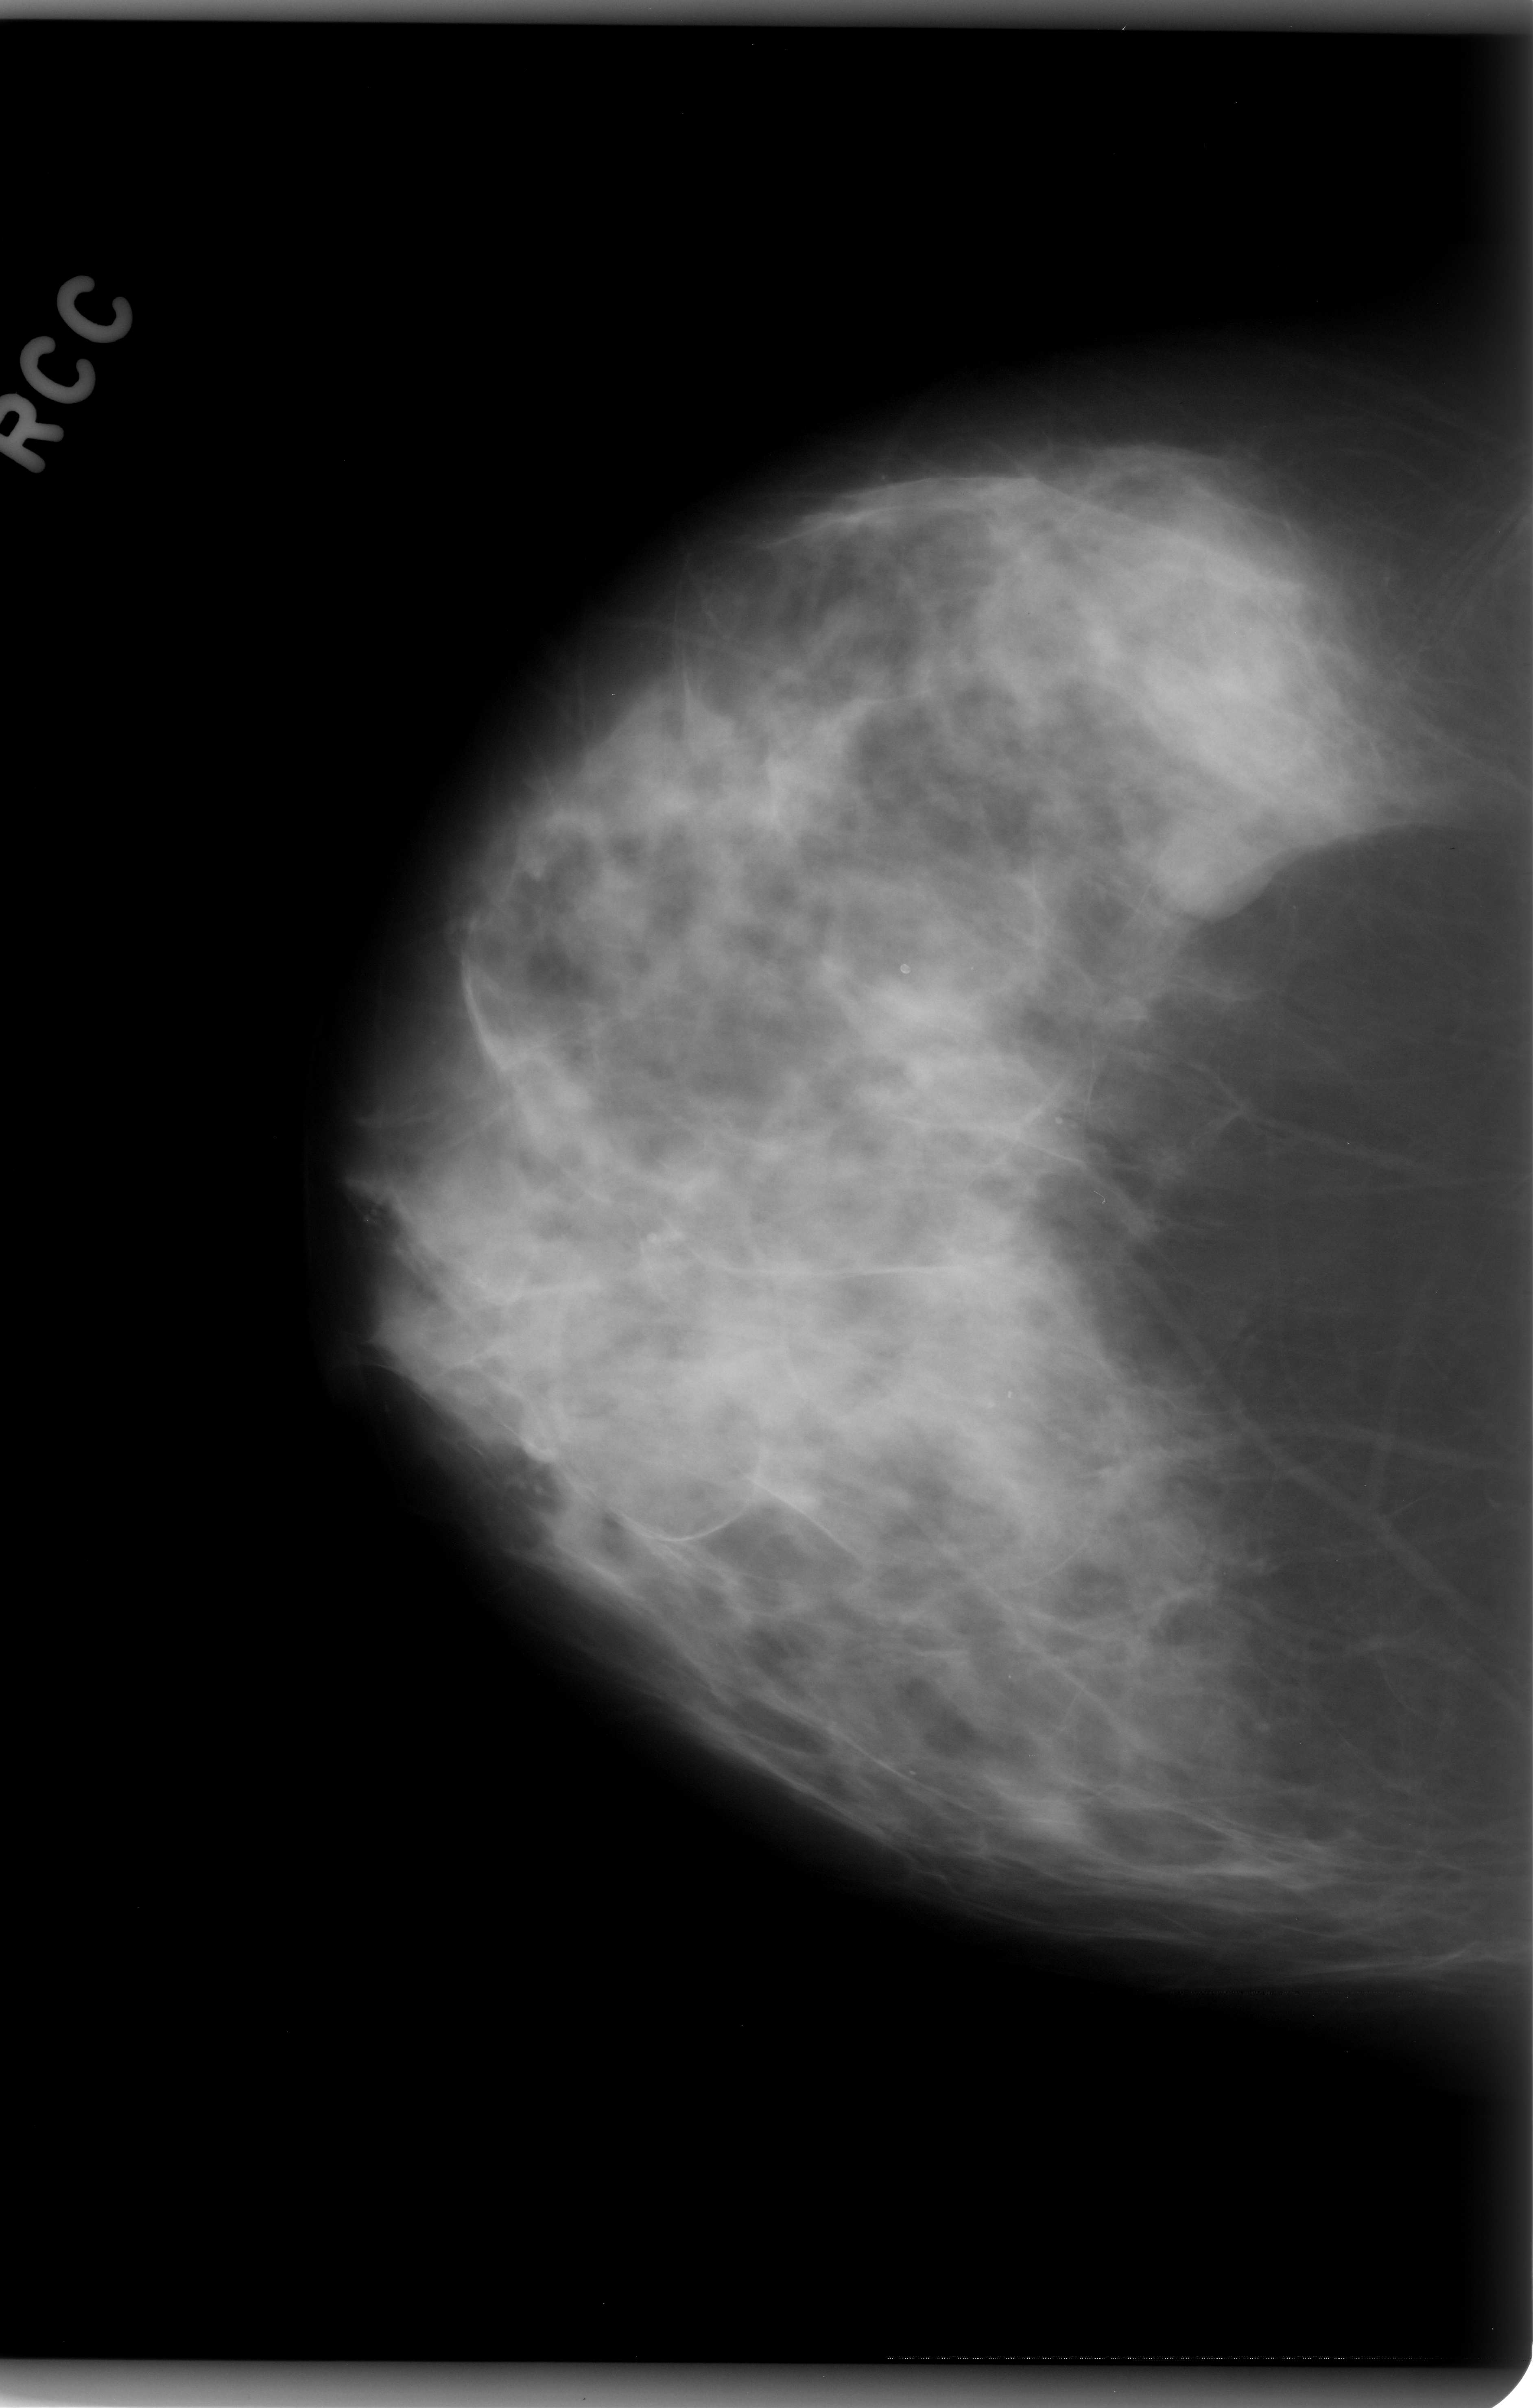
Scanned film-screen mammogram, right breast, CC view, BI-RADS breast density category 3 (scale 1–4).
Finding: mass, shape oval, margins circumscribed; BI-RADS assessment category 4; subtlety rating 5 on a 1 (subtle) to 5 (obvious) scale; pathology (as recorded): benign.